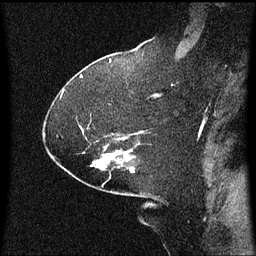
Breast MRI (dynamic contrast-enhanced), one sagittal slice. Position 39 of 60 along the scan axis. Dynamic contrast-enhanced series, image 2 of 3 at this slice position (ordered by acquisition). 1.5 T. TE 4.2 ms, TR 8 ms. 2.1 mm slice thickness. 256 × 256 image matrix. Female patient, age 59 years.
Outlined on this slice (semi-automatically segmented with operator editing):
- analysis volume of interest (the breast-tissue region the enhancement analysis was run in; not a lesion): bounding box [x1, y1, x2, y2] px = [84, 150, 135, 173]
- tumour enhancement mask (voxels above the 70 % enhancement threshold inside the analysis volume of interest): [92, 150, 131, 167]